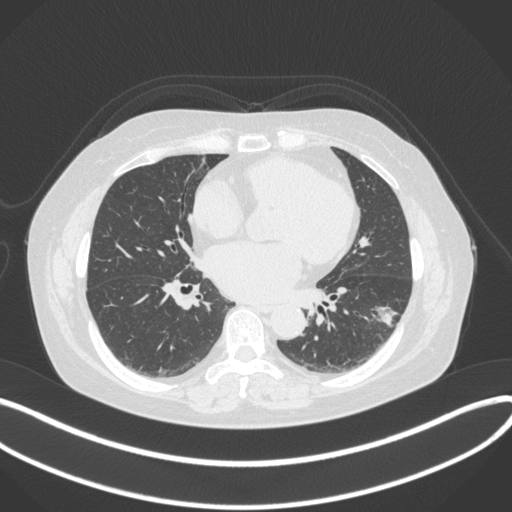
Chest CT, one axial slice; 120 kVp; lung window (W 1500 / L -600 HU); 1 mm slice thickness; 512 × 512 image matrix, field of view 400 × 400 mm. Patient: female, 67 years. Case-level facts recorded for this patient, not image findings: clinical TNM (as recorded): T1c N0 M0.
Outlined on this slice (bounding box drawn by a radiologist):
- lung tumour (recorded histology: adenocarcinoma): box from (x=365, y=301) to (x=401, y=331) px